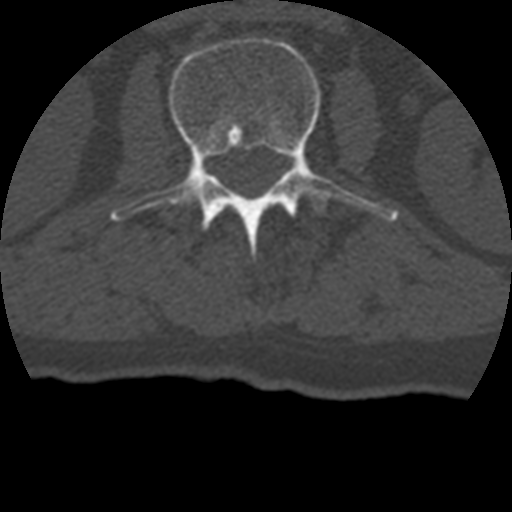
CT including the spine, one axial slice; slice 118 of 399 in the series (ordered by position); bone window (W 1800 / L 400 HU); 1.25 mm slice thickness; 512 × 512 image matrix, field of view 160 × 160 mm. Patient age 69 years. Case-level facts recorded for this patient, not image findings: primary cancer: prostate.
Structures marked on this image (semi-automatically segmented with operator editing):
- L2 vertebra: box from (x=111, y=36) to (x=397, y=258) px